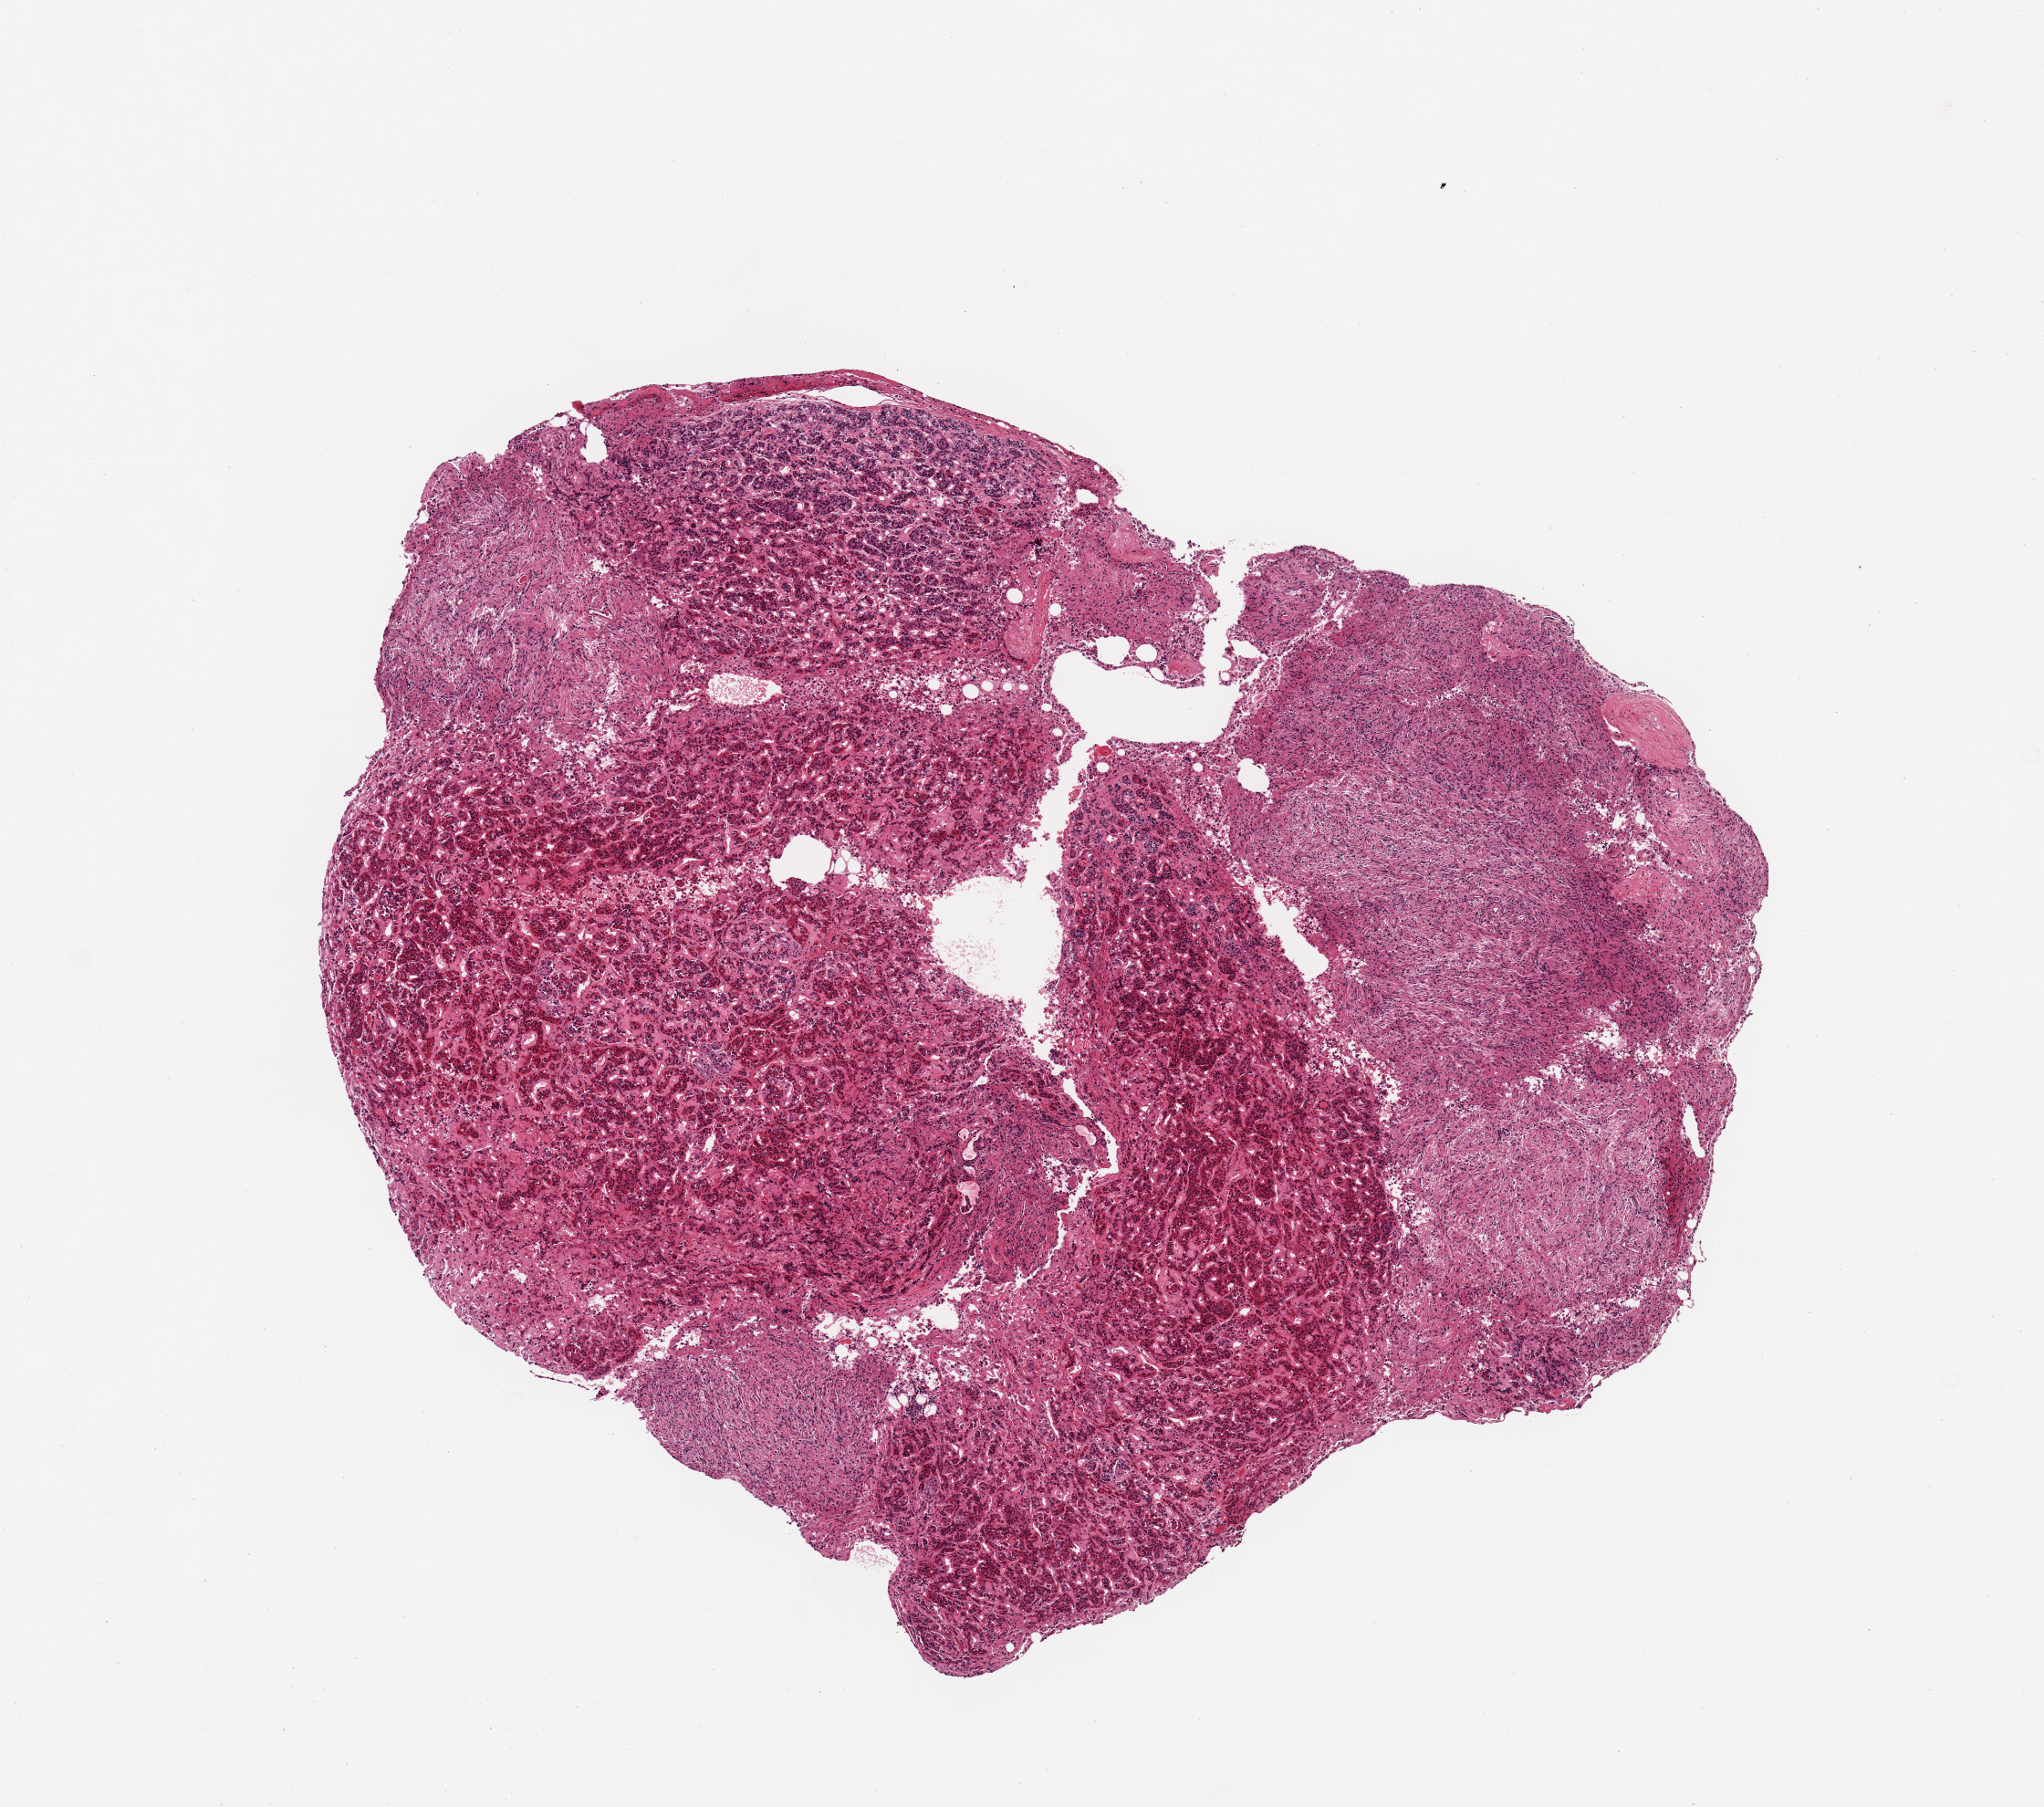
Whole-slide image, H&E stain, brightfield — shown as a low-resolution overview of the whole scanned area (about 8.9 x 7.8 mm); PAXgene-fixed, paraffin-embedded tissue; sampled site (target tissue): pituitary; tissue donor sample. Donor: male.
Reviewer comment on this tissue sample: 1 piece; foci of posterior pituitary, comprise 30%.